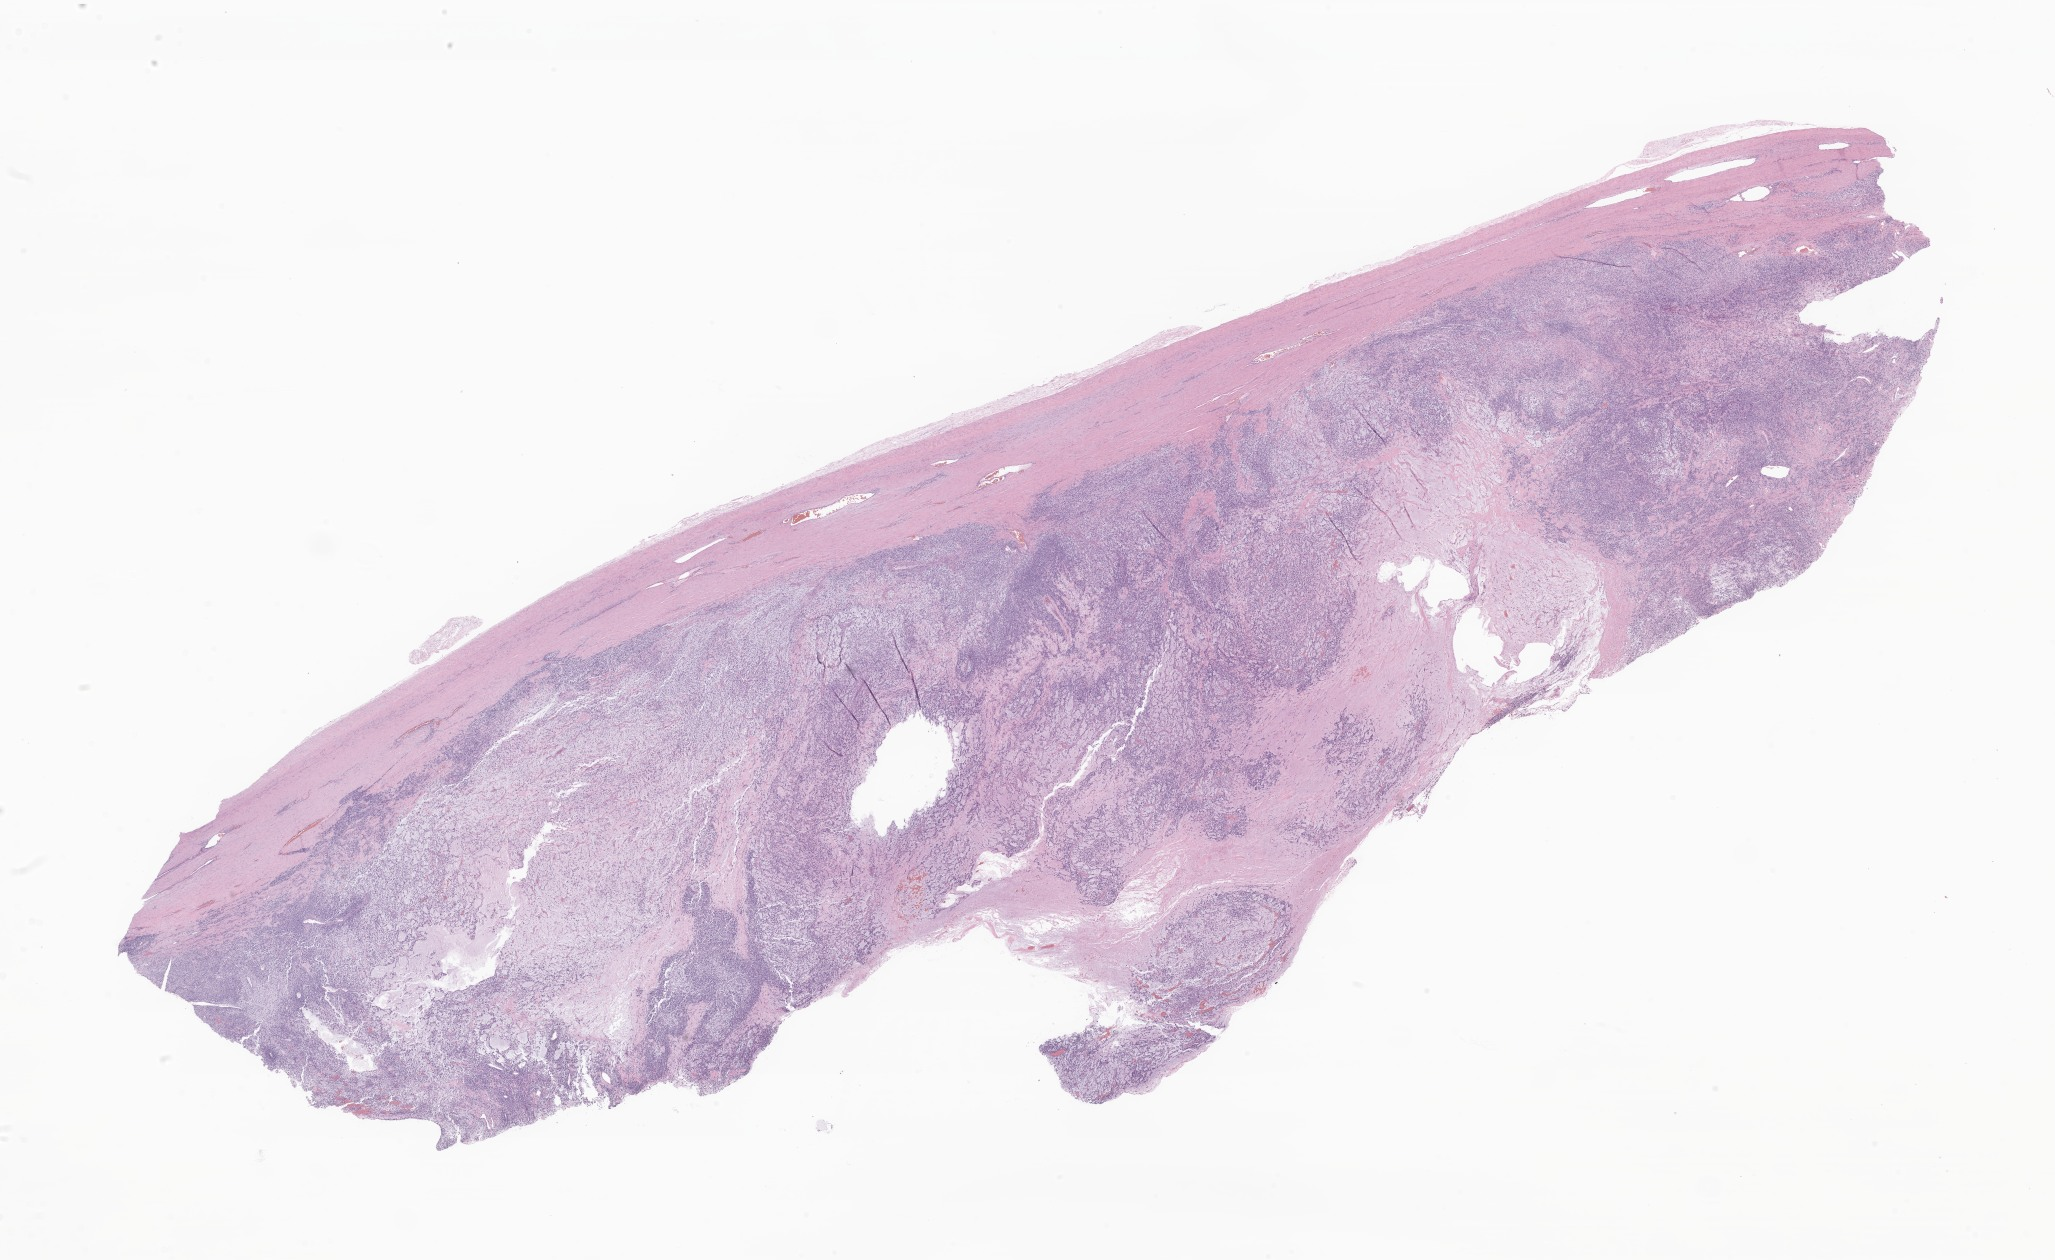
Digitized haematoxylin and eosin-stained section of tumor tissue from the testis — a low-resolution overview of the entire scanned area, about 34.7 x 21.2 mm. FFPE section. Patient: male, age 201 months (16 years 9 months).
Diagnosis (ICD-O-3 morphology term): Embryonal rhabdomyosarcoma, NOS.